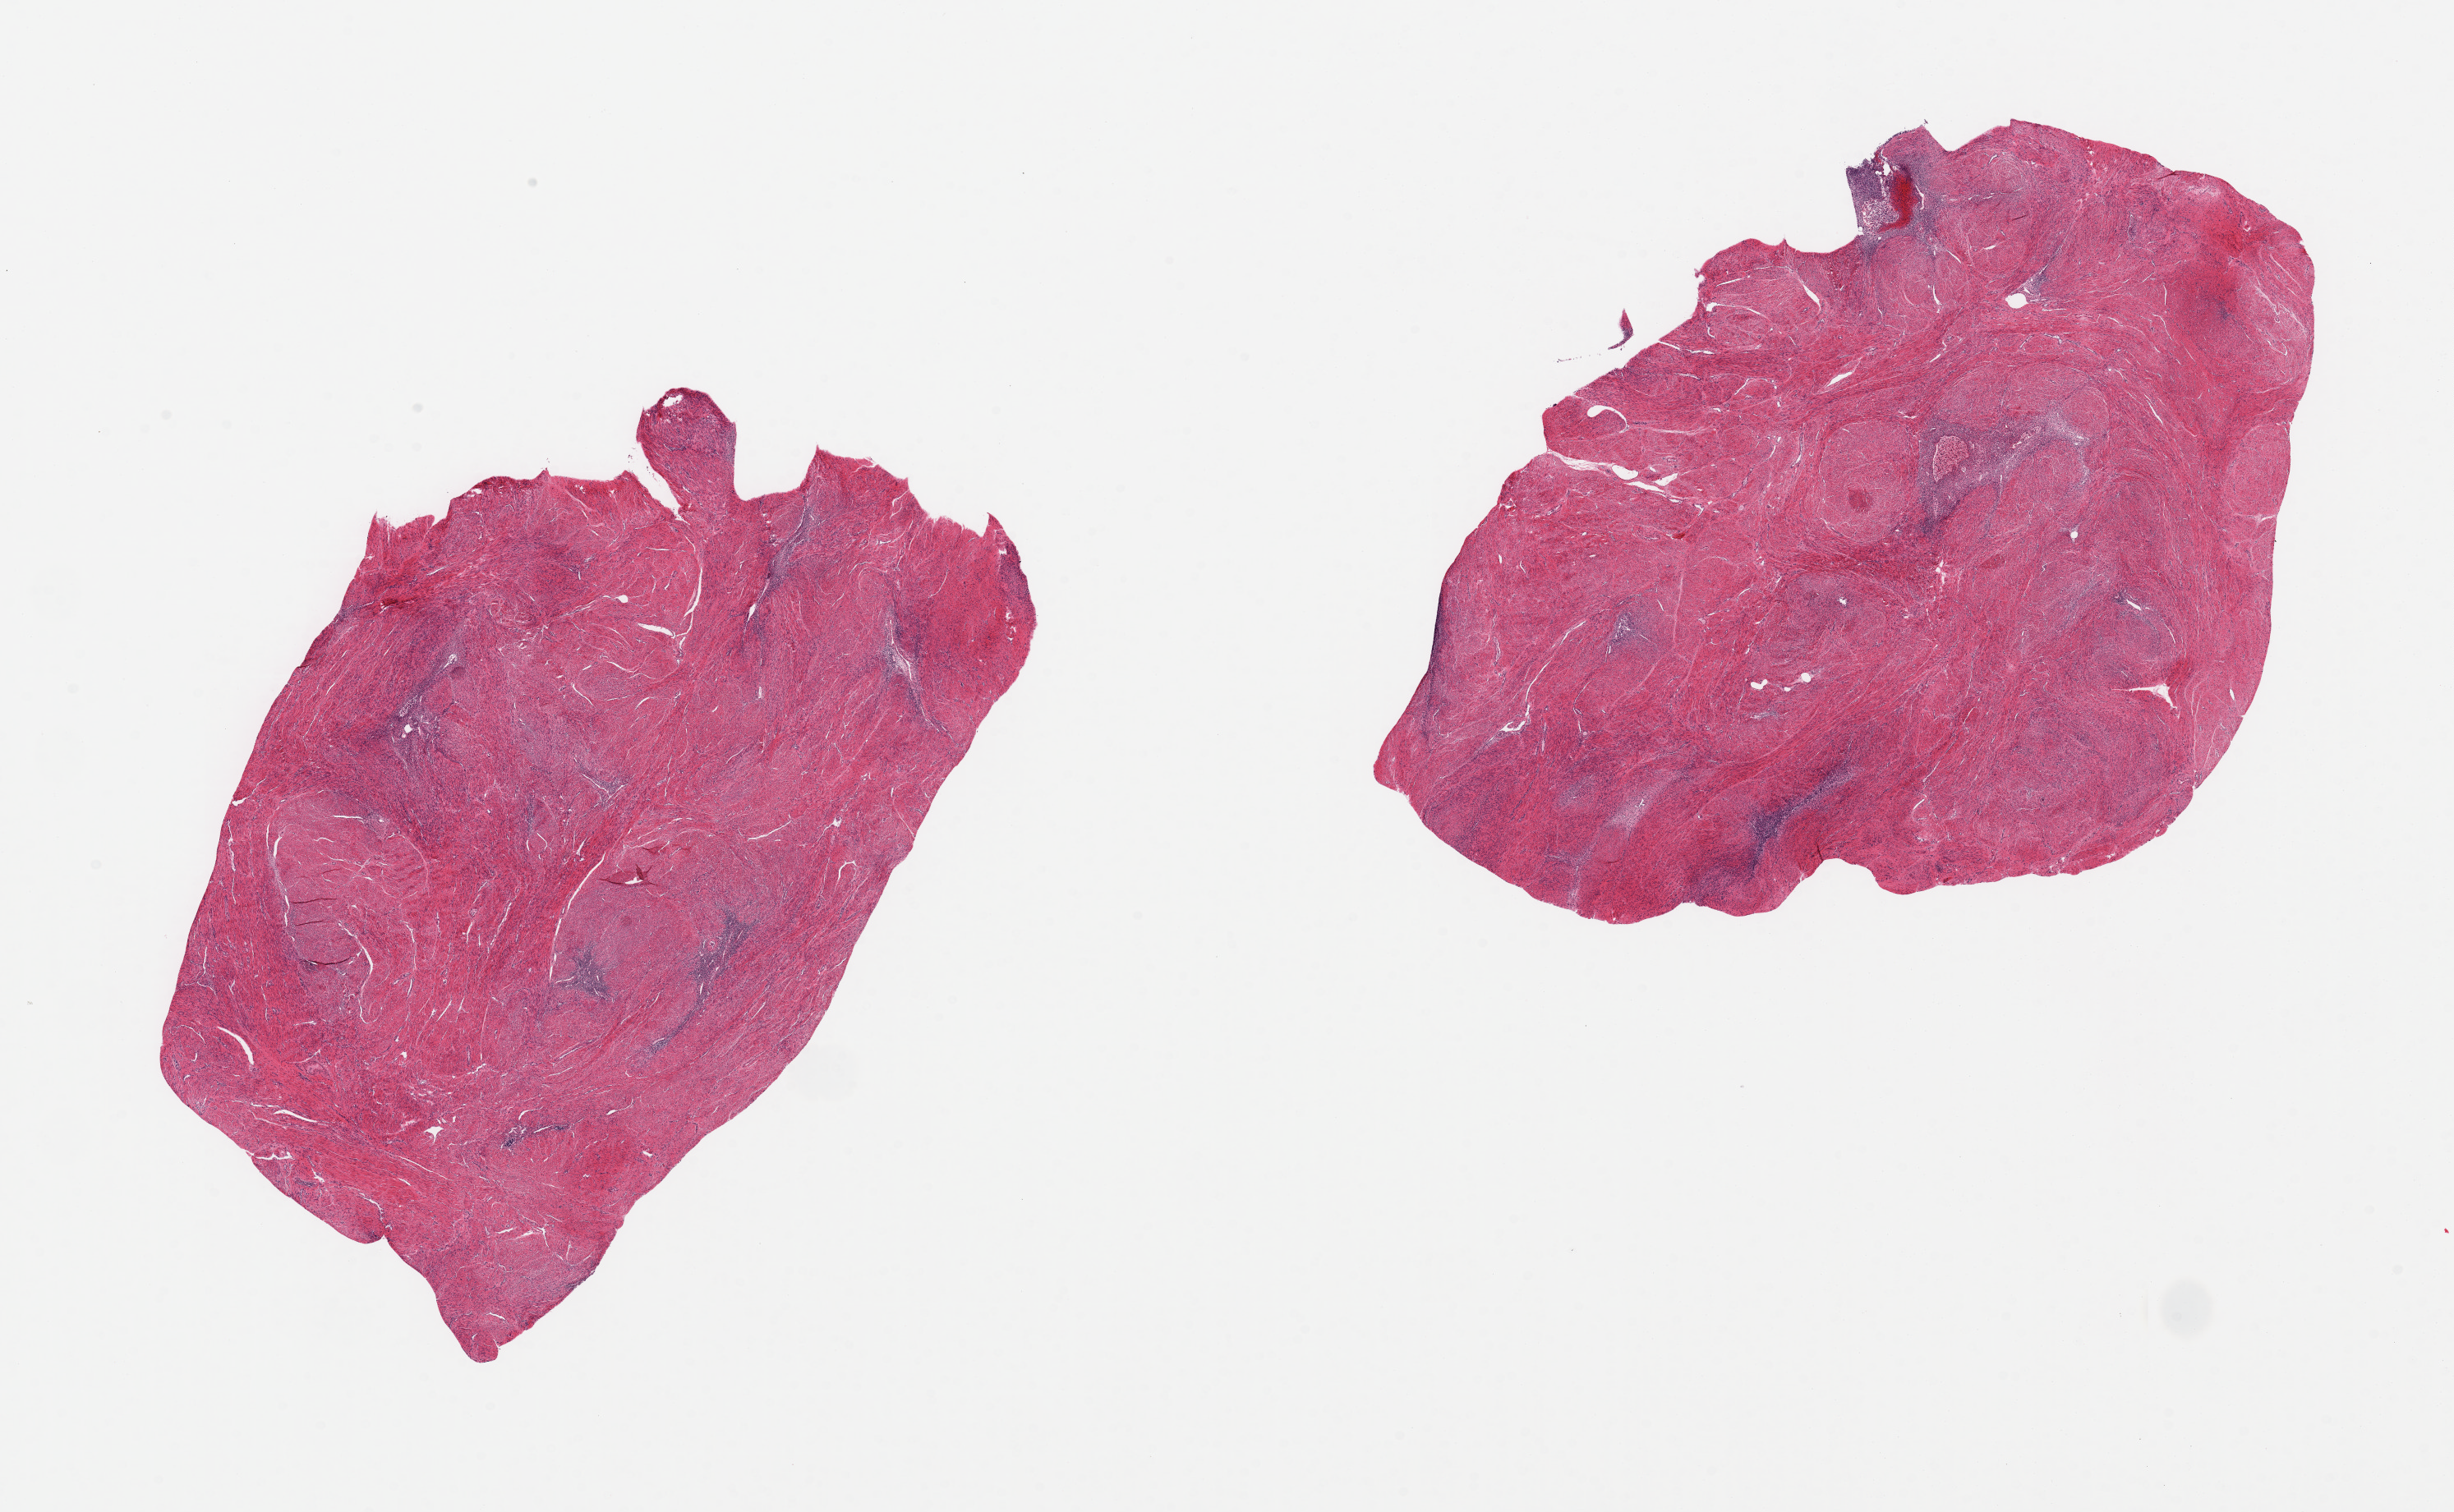
Digitized haematoxylin and eosin-stained section, low-resolution overview of the scanned area, about 23.6 x 14.6 mm, PAXgene-fixed paraffin-embedded (PFPE) section, sampled site (target tissue): uterus, tissue donor sample.
Review note (as recorded): 2 pieces, mainly myometrium, foci of of autolyzed adenomyosis.